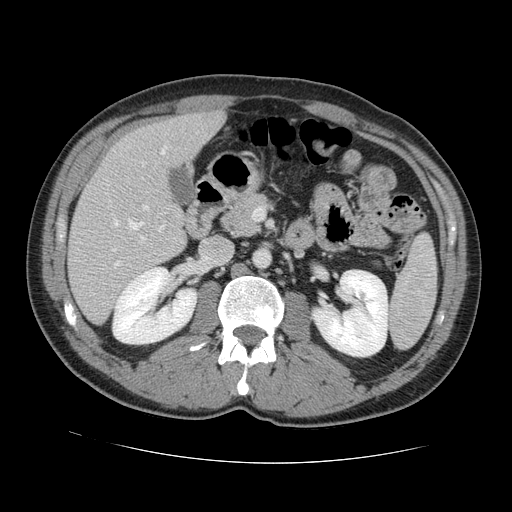
Contrast-enhanced abdominal CT, one axial slice; position 63 of 131 along the scan axis; 120 kVp; intravenous contrast given; soft-tissue window (W 400 / L 40 HU); 512 × 512 image matrix, field of view 380 × 380 mm. Male patient, age 40 years. From the clinical record (not read from this slice): diagnosis: colorectal cancer liver metastases, imaged before liver resection; multiple liver metastases: yes; largest metastasis: 2.9 cm; disease in both lobes: yes.
Outlined on this slice (manually delineated by an expert):
- hepatic veins: bounding box <113,145,167,251> (left, top, right, bottom; pixels)
- liver: <68,113,222,323>
- planned liver remnant (the part of the liver to remain after resection): <110,113,222,180>
- portal vein (with intrahepatic branches): <114,205,164,267>